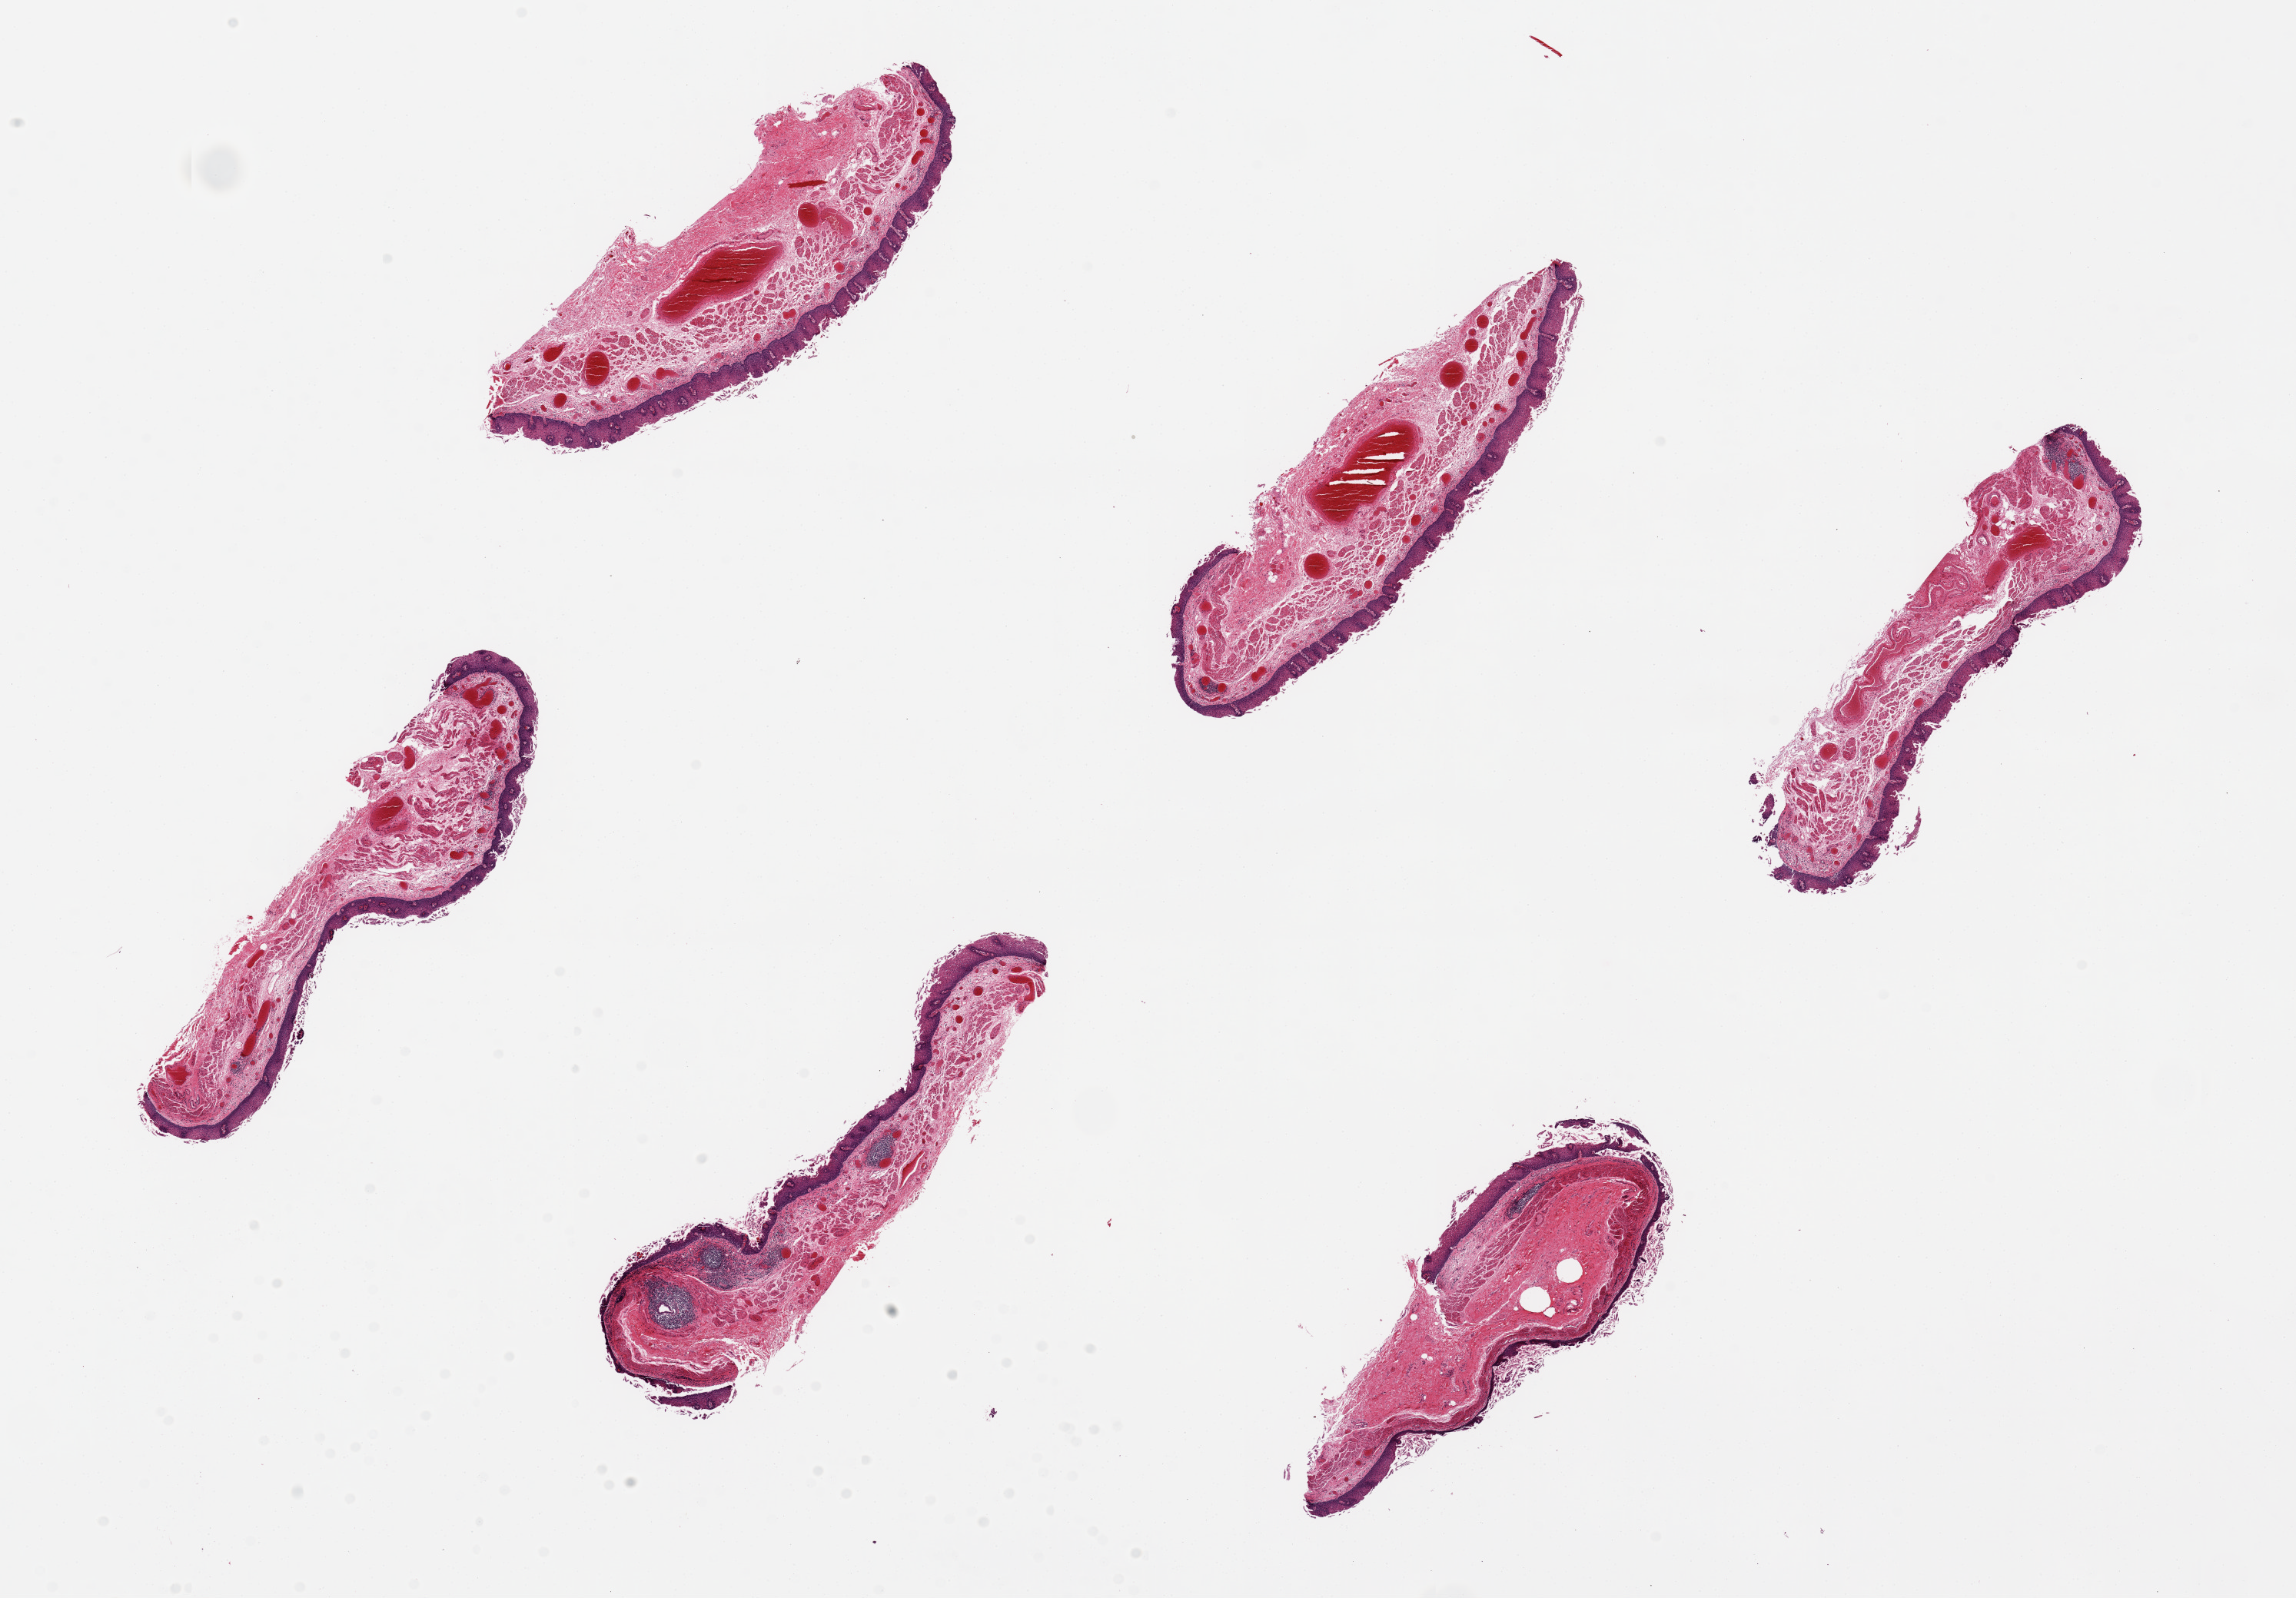
Digitized H&E-stained section, whole scanned area (about 23.6 x 16.4 mm) shown as a low-resolution overview; PAXgene-fixed, paraffin-embedded tissue; target tissue: esophageal mucous membrane; donor tissue sample. Donor: male.
Pathologist's review note for this sample: 6 pieces. up to 6x2mm; squamous mucosa is ~10% thickness.